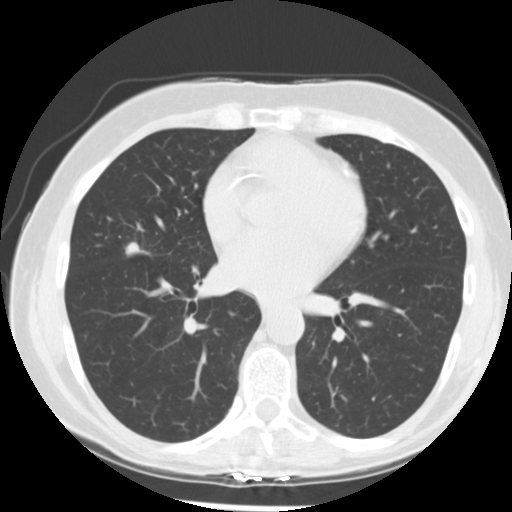
Low-dose screening chest CT, one axial slice; slice 128 of 255 in the series (ordered by position); reconstruction kernel STANDARD; 120 kVp; lung window (W 1500 / L -600 HU); 512 × 512 image matrix, field of view 320 × 320 mm.
Outlined on this slice (outlined manually by an expert reader):
- lesion 1 (tumor, middle lobe of right lung): box from (x=126, y=242) to (x=140, y=256) px